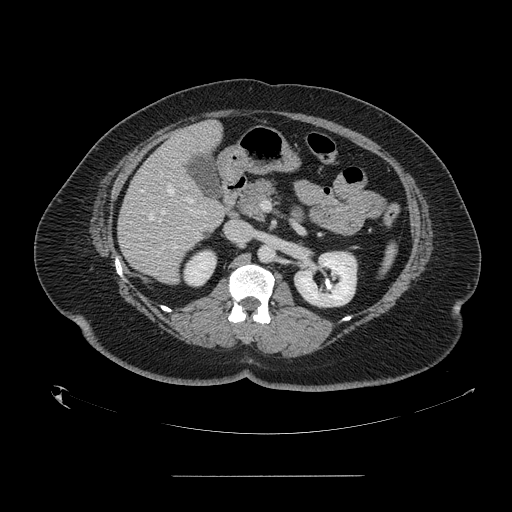
Contrast-enhanced abdominal CT, one axial slice. Position 74 of 164 along the scan axis. 120 kVp. Soft-tissue window (W 400 / L 40 HU). 2.5 mm slice thickness. 512 × 512 image matrix, field of view 495 × 495 mm. Female patient, age 52 years. From the clinical record (not read from this slice): diagnosis: colorectal cancer liver metastases, imaged before liver resection; multiple liver metastases: yes.
Outlined on this slice (expert manual segmentation):
- hepatic veins: bounding box <148,188,197,220> (left, top, right, bottom; pixels)
- liver: <118,122,226,283>
- planned liver remnant (the part of the liver to remain after resection): <177,122,222,157>
- portal vein (with intrahepatic branches): <161,175,192,203>
- liver metastasis: <203,229,211,238>